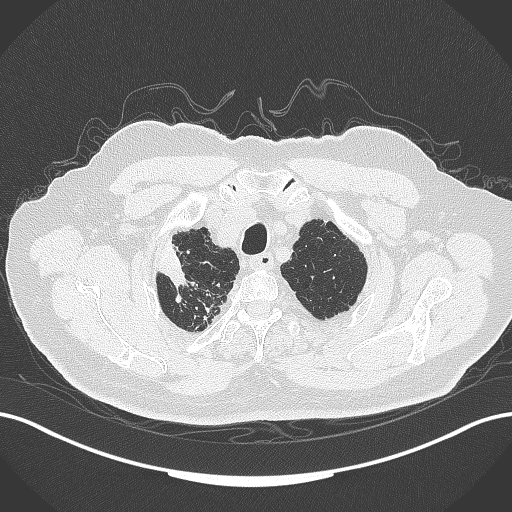
Chest CT, one axial slice. Reconstruction kernel B70f. Lung window (W 1500 / L -600 HU). 512 × 512 image matrix, field of view 400 × 400 mm. Male patient, age 72 years. Case-level facts recorded for this patient, not image findings: clinical TNM (as recorded): T1a N0 M0.
Structures marked on this image (bounding box drawn by a radiologist):
- lung tumour (recorded histology: squamous cell carcinoma): bounding box (x1, y1, x2, y2) in pixels: (155, 235, 190, 284)